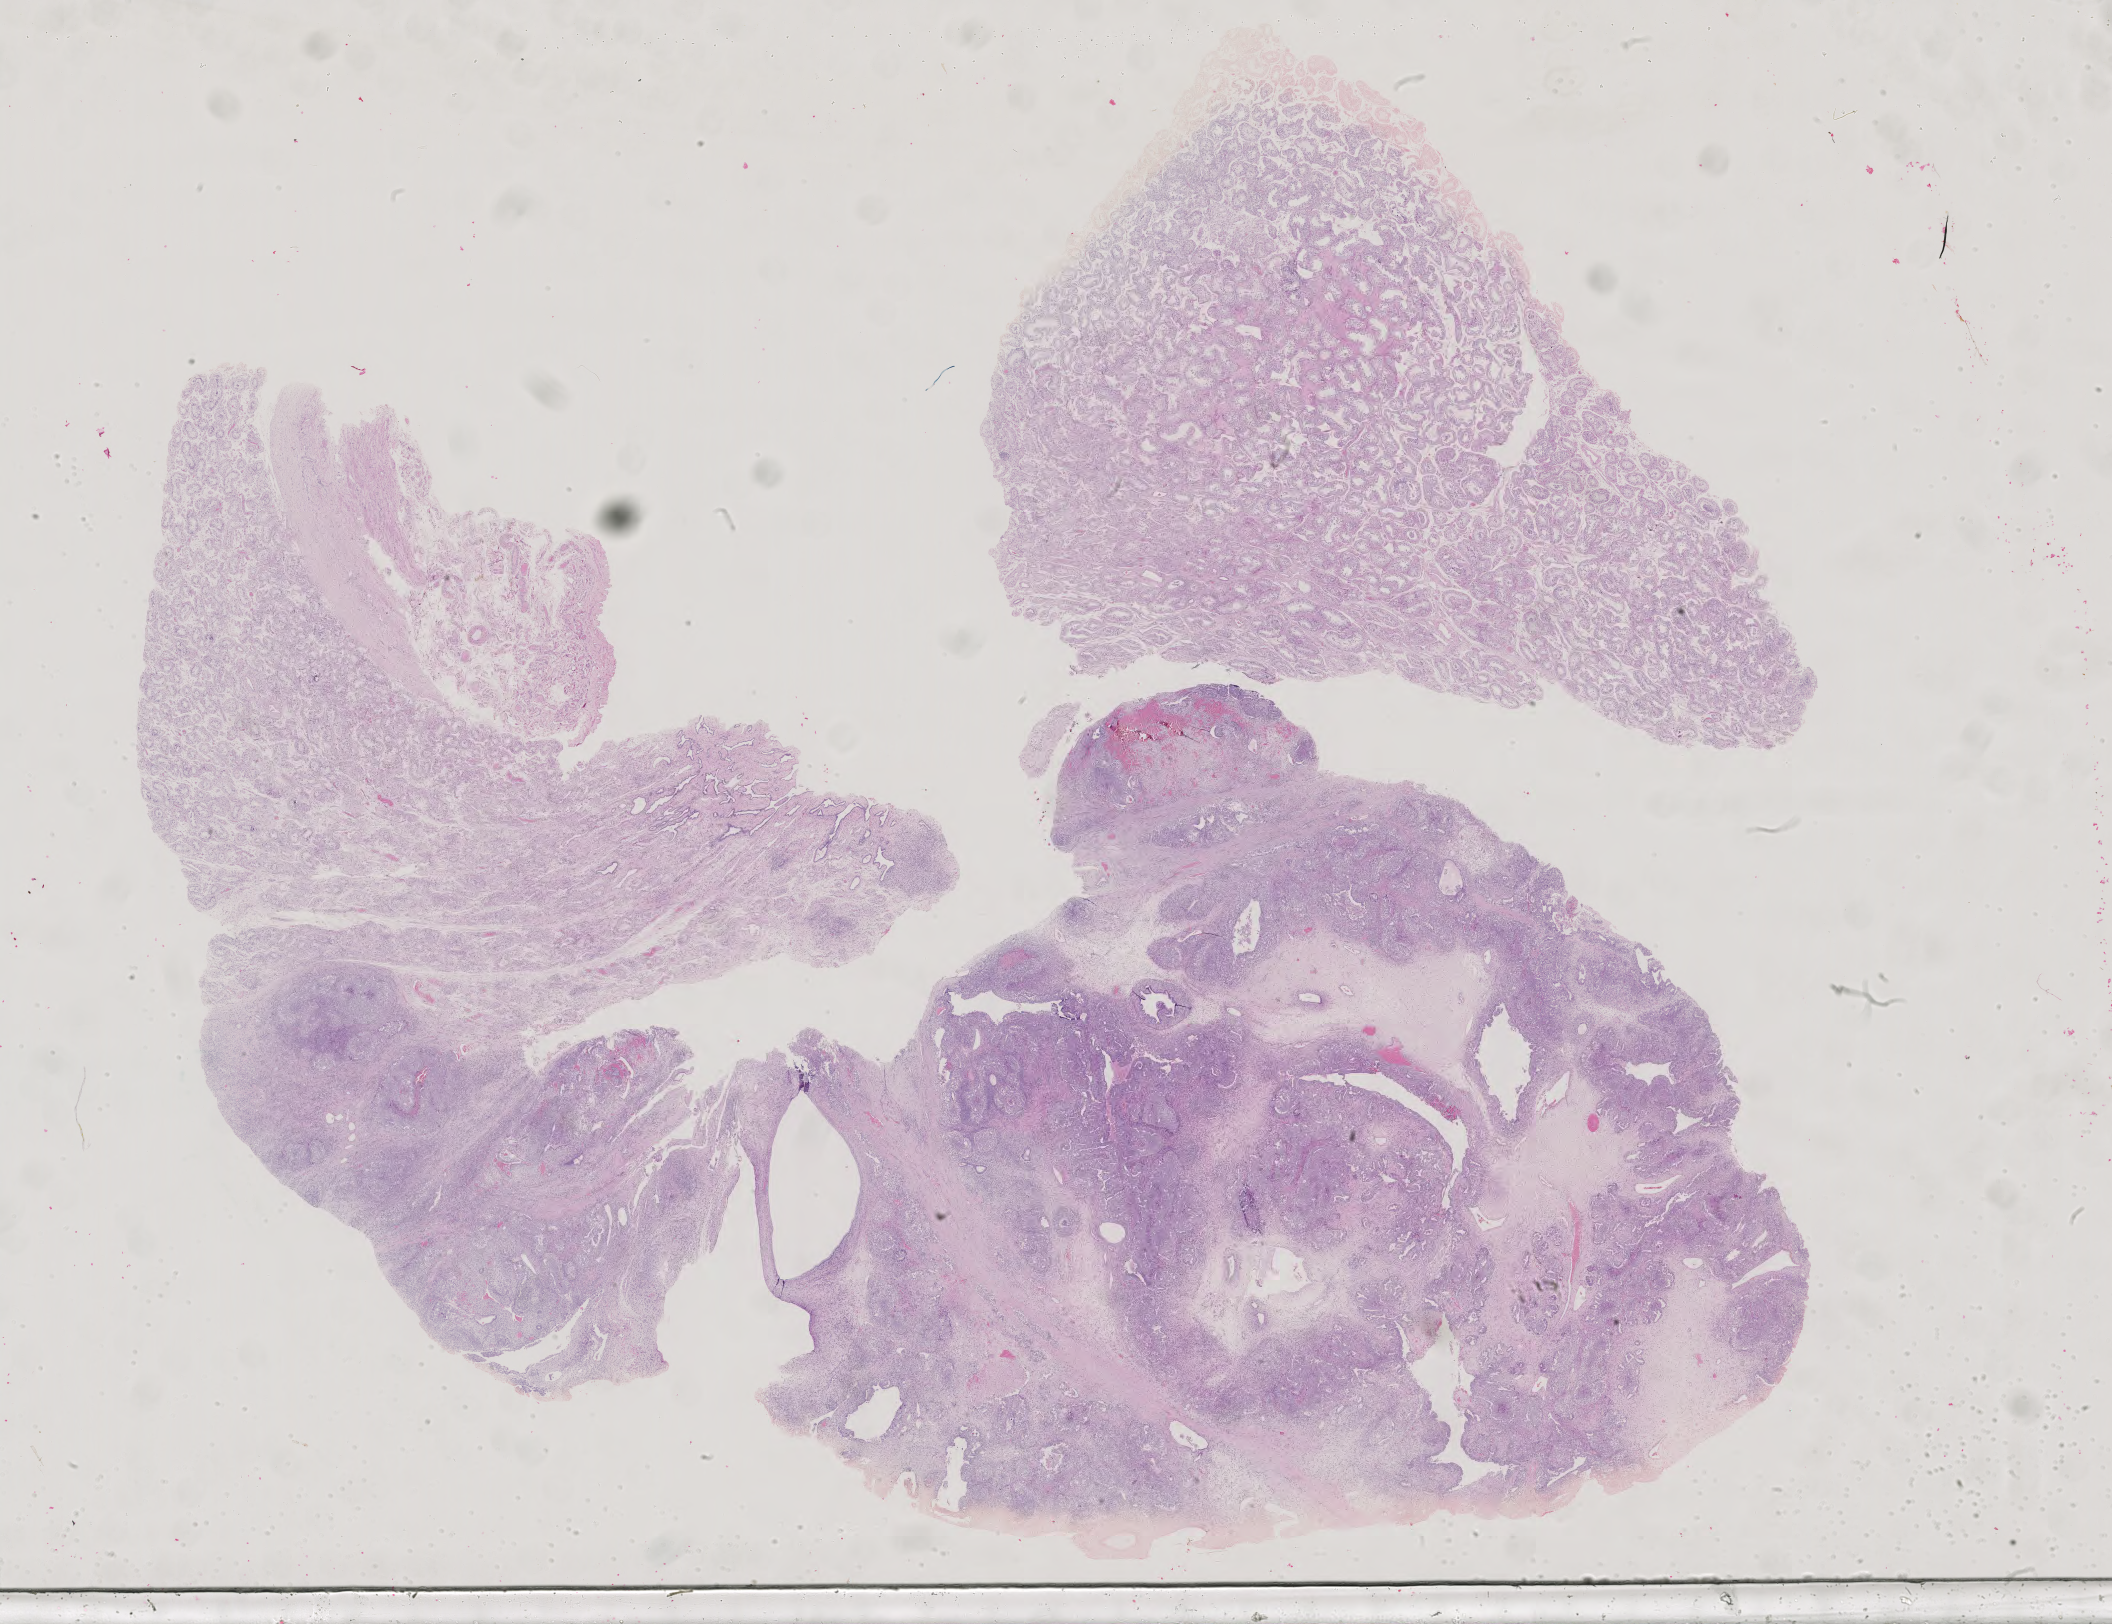
H&E whole-slide image — shown as a low-resolution overview of the whole scanned area (about 30.8 x 23.7 mm). Formalin-fixed paraffin-embedded (FFPE) diagnostic section. Testis, primary tumour sample. Male patient; age at initial diagnosis 33 years.
• TNM: T2 N1 M0
• AJCC pathologic stage: IIA (6th edition)
• histologic diagnosis: Mixed germ cell tumor